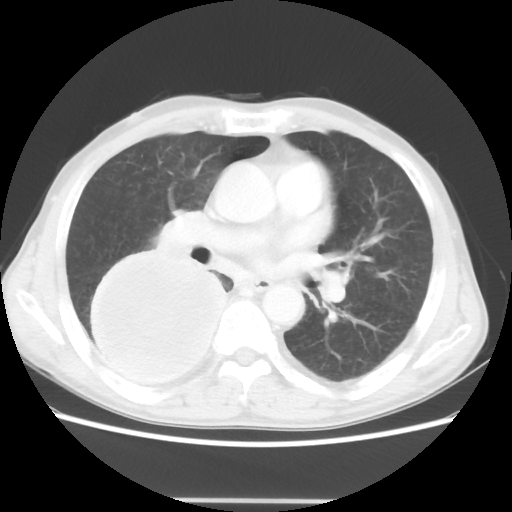
Chest CT, one axial slice; reconstruction kernel STANDARD; 100 kVp; lung window (W 1500 / L -600 HU); 512 × 512 image matrix, field of view 361 × 361 mm. Patient: male, 66 years. From the clinical record (not read from this slice): clinical TNM (as recorded): T4 N1 M1; histopathological grade: G3.
Structures marked on this image (bounding box drawn by a radiologist):
- lung tumour (recorded histology: small cell carcinoma): bounding box <89,250,238,388> (left, top, right, bottom; pixels)